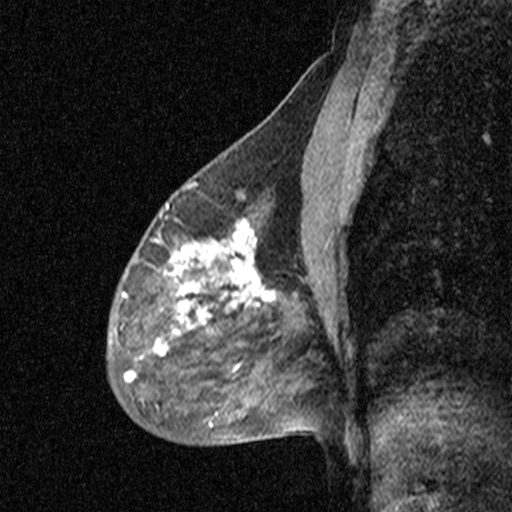
Breast MRI (dynamic contrast-enhanced), one sagittal slice. Position 26 of 44 along the scan axis. Dynamic contrast-enhanced study with each time point stored as its own series, time point 2 of 3 at this slice position (early post-contrast, ordered by acquisition time). 1.5 T. TE 4.5 ms, TR 11 ms. 3 mm slice thickness. 512 × 512 image matrix, field of view 200 × 200 mm. Patient: female, 53 years. Case-level facts recorded for this patient, not image findings: setting: breast cancer imaged before/during neoadjuvant chemotherapy; receptor status: HR-positive, HER2-negative.
Annotated regions visible in this slice (semi-automatically segmented with operator editing):
- analysis volume of interest (the breast-tissue region the enhancement analysis was run in; not a lesion): box from (x=88, y=176) to (x=313, y=423) px
- tumour enhancement mask (voxels above the 90 % enhancement threshold inside the analysis volume of interest): (x=123, y=192)–(x=275, y=380)